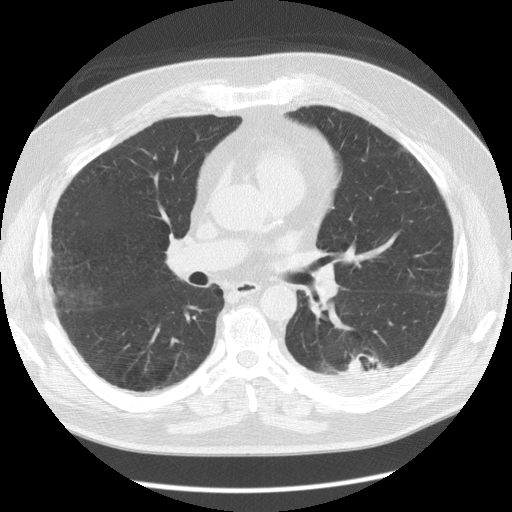
Low-dose screening chest CT, axial slice; first (baseline) screen; lung window (W 1500 / L -600 HU); 2.5 mm slice thickness; 120 kVp; 512 × 512 image matrix, field of view 370 × 370 mm. Male participant, aged 56 years at enrolment. Former smoker at enrolment.
- Lesion marked by an expert reader, bounding box [x1, y1, x2, y2] px = [323, 339, 395, 392].
- The screening reader recorded 4 non-calcified nodules or masses ≥4 mm on this exam; which of them this box marks is not recorded.
- Official screen result: positive, change unspecified: nodule(s) >= 4 mm or enlarging nodule(s), mass(es), or other non-specific abnormalities suspicious for lung cancer.
- Later outcome: lung cancer diagnosed 173 days after this screen — non-small cell carcinoma, left lower lobe, stage IV (AJCC 6th edition), 50 mm at pathology.